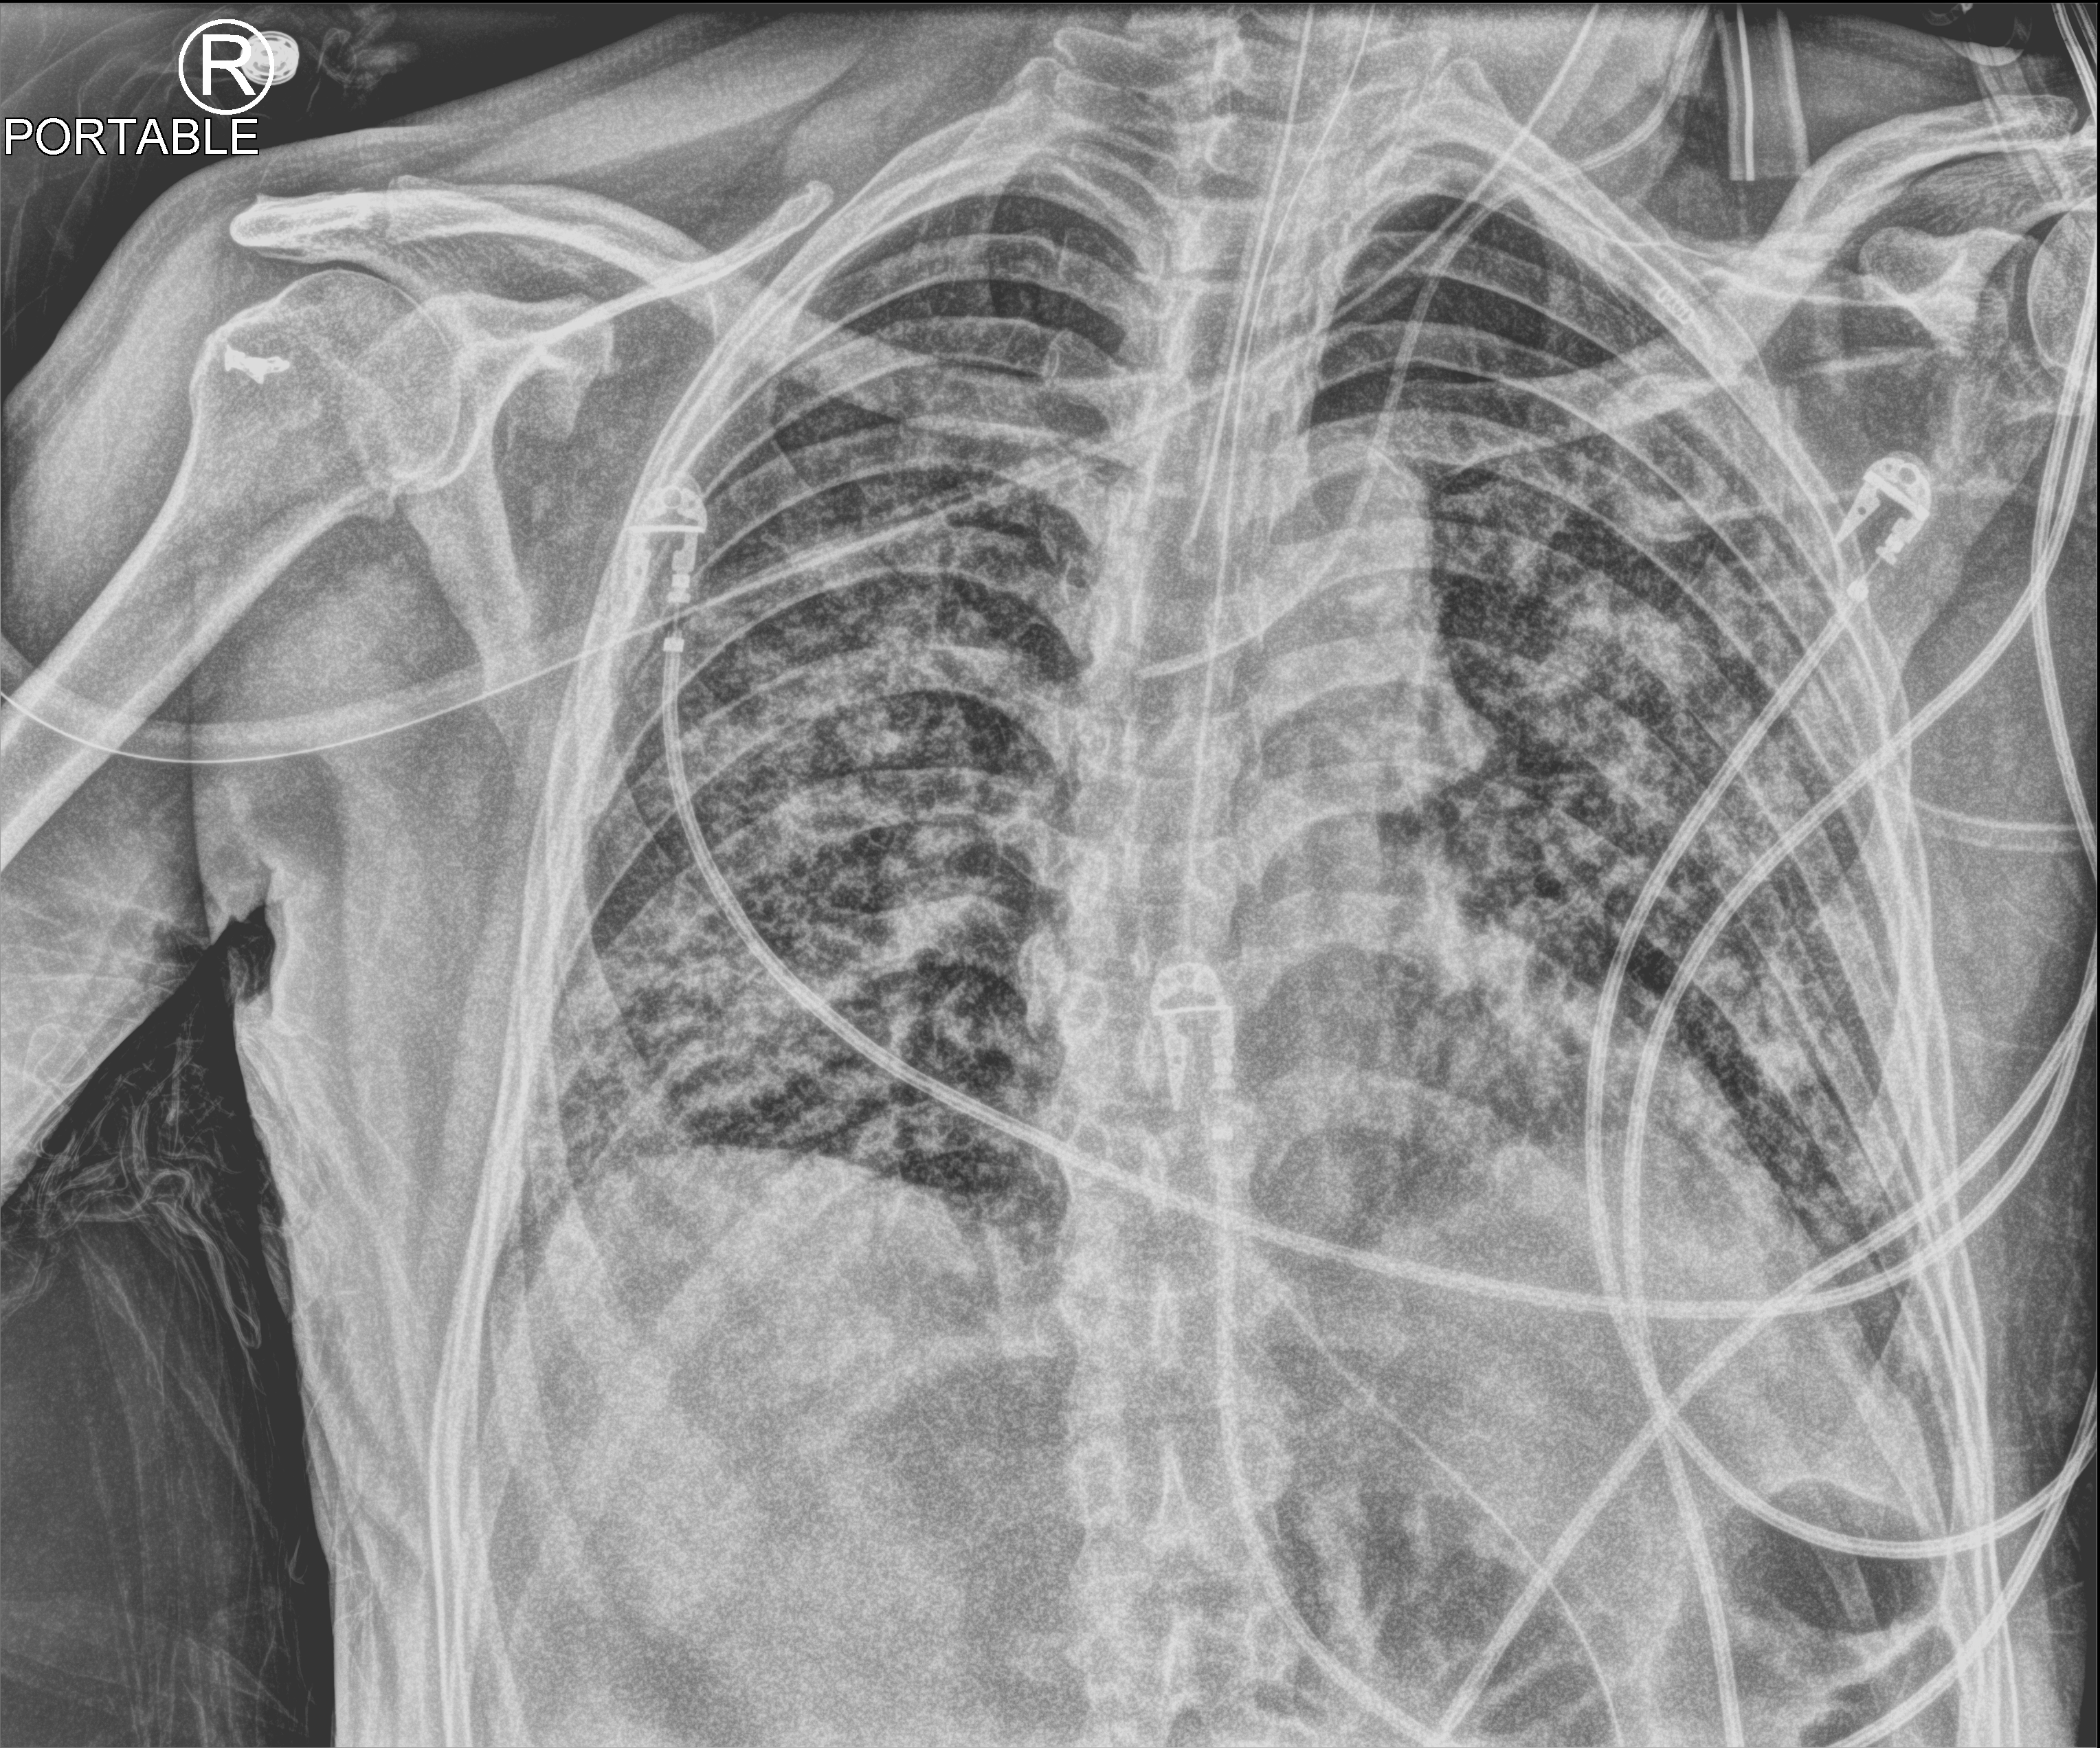
Portable chest radiograph, anteroposterior (AP) projection. Male patient hospitalised with COVID-19, age 60–74 years.
Admission-level facts for this patient (not findings on this image; timing relative to this image not recorded): diabetes (admission record): no; other chronic lung disease (admission record): yes.